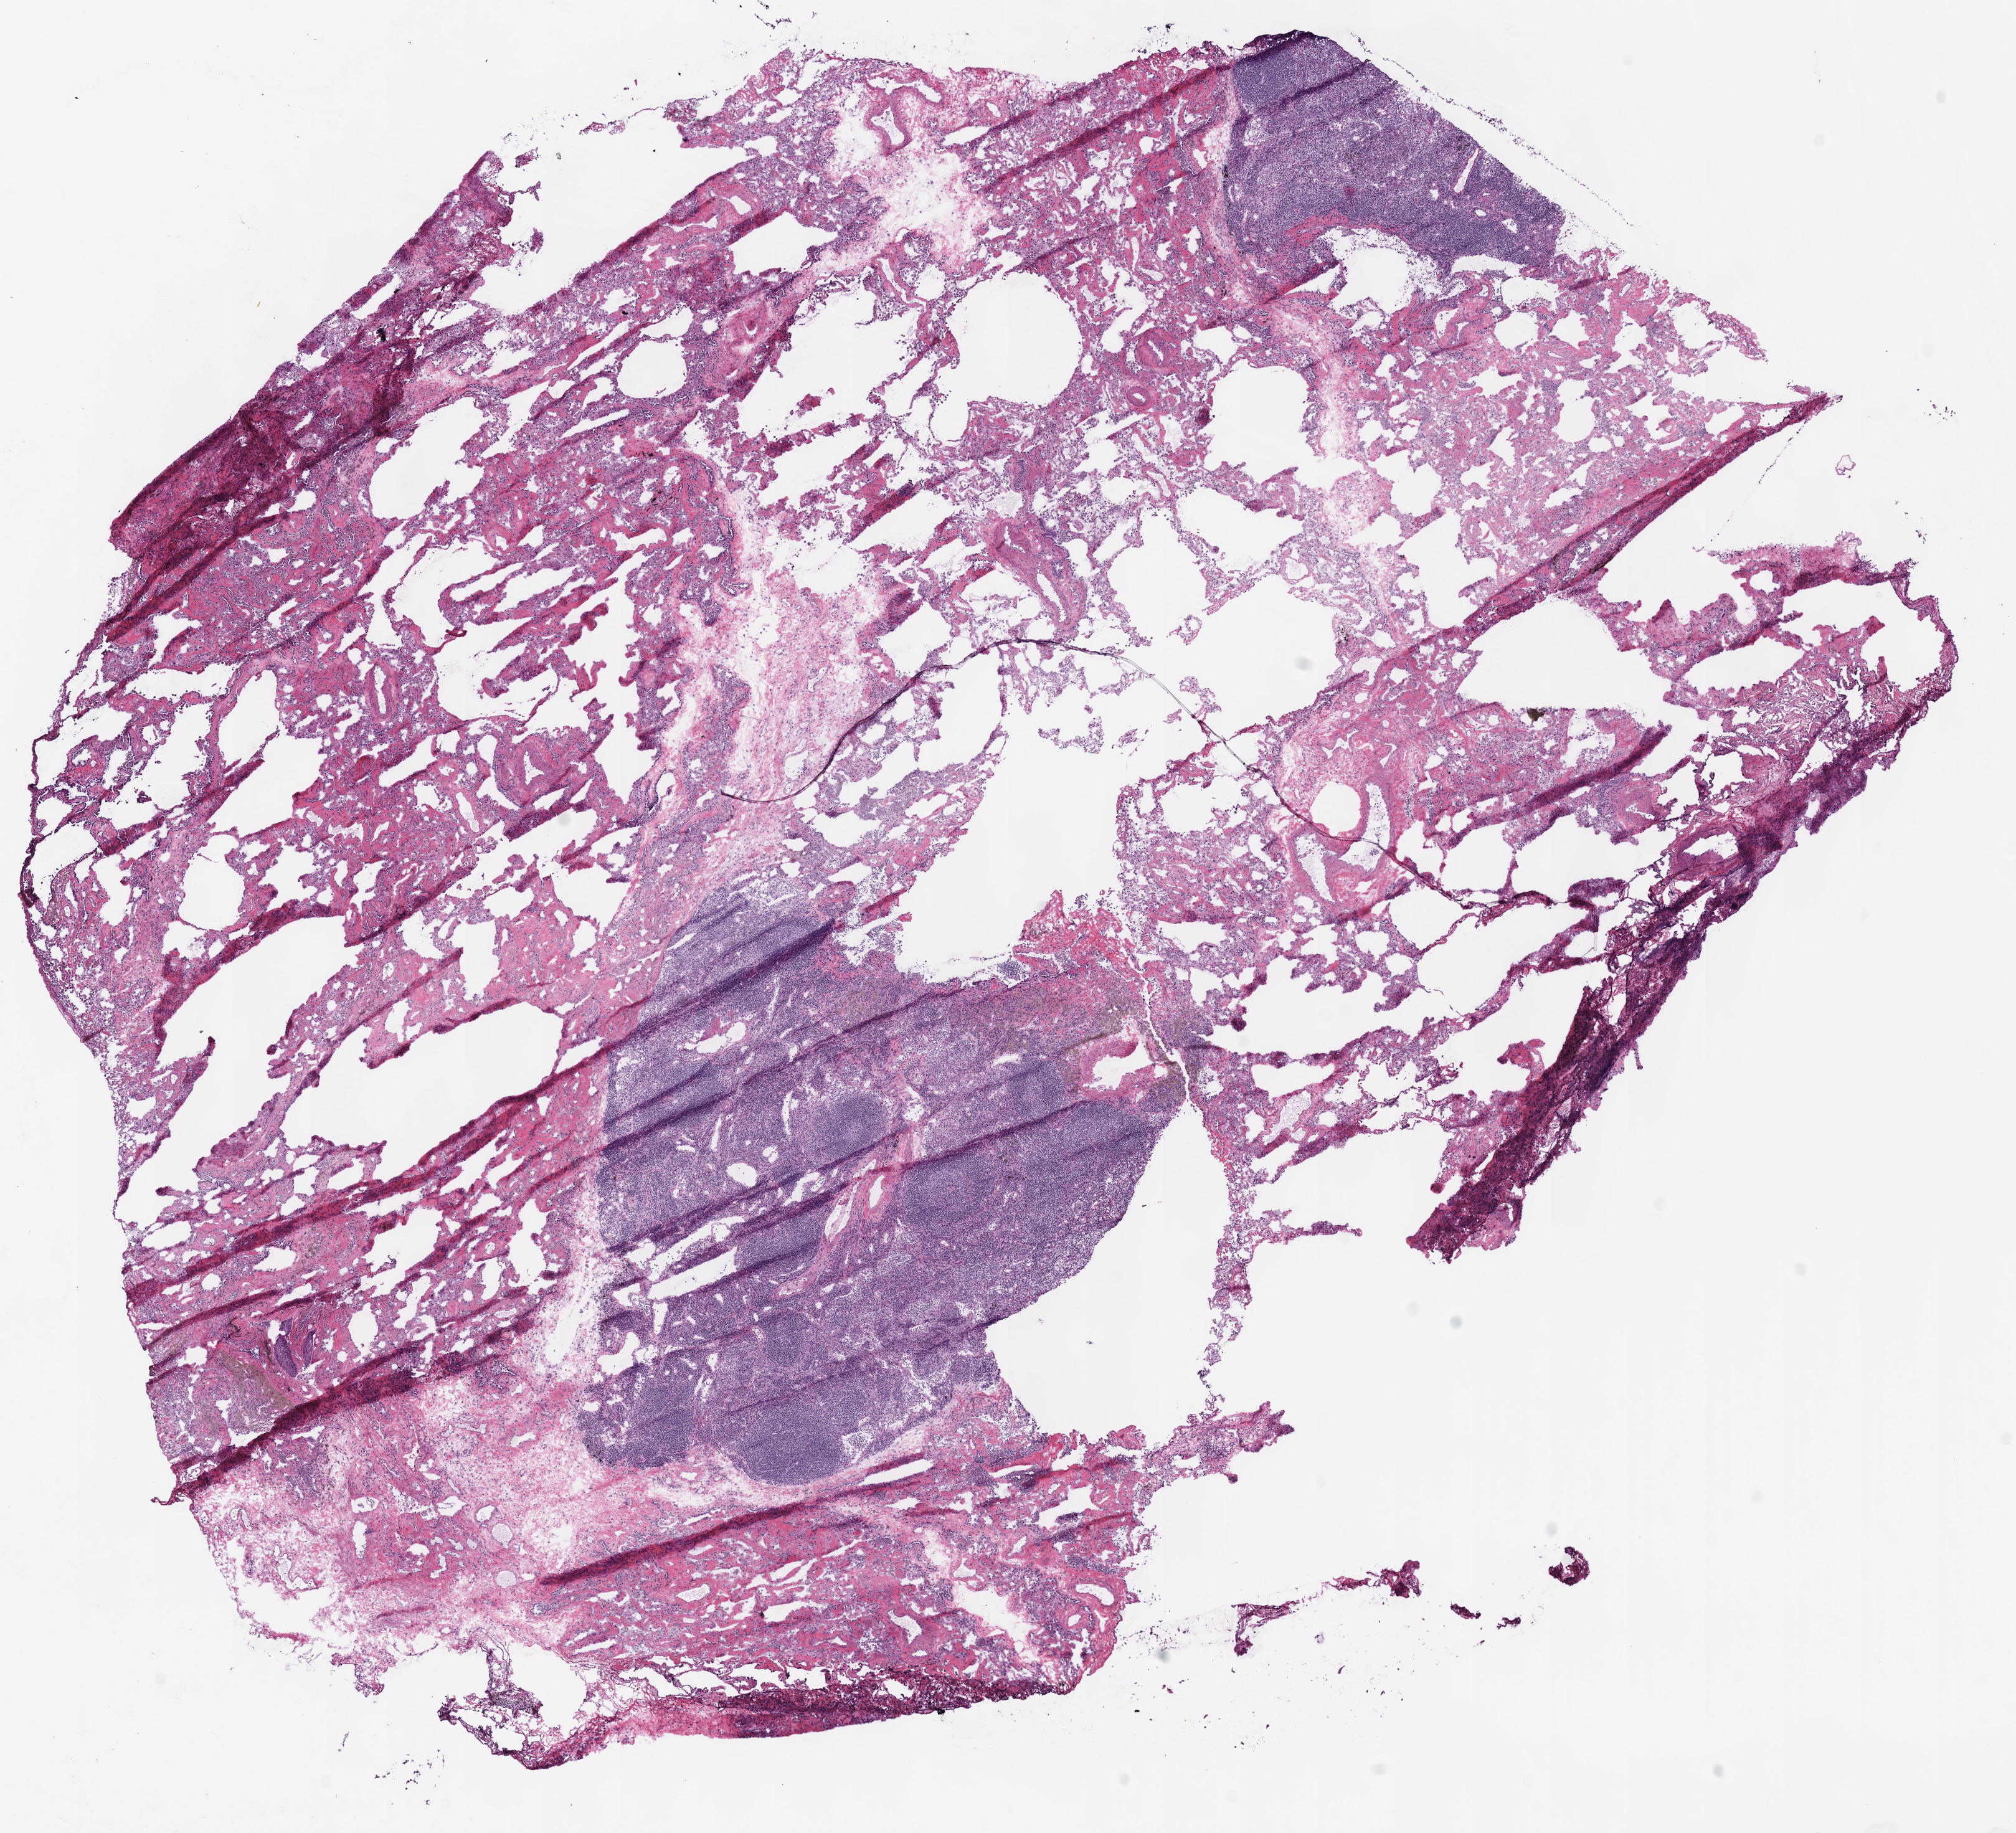
Digitized Hematoxylin and eosin (H&E) stained tissue section (whole slide), shown as a low-resolution overview of the whole scanned area (about 12.7 x 11.6 mm). Frozen section from the top of the tissue portion. Lung, solid tissue normal (non-tumour tissue) sample. Female patient; age at initial diagnosis 59 years. Inflammatory infiltration, as recorded: lymphocyte infiltration 35%, monocyte infiltration 20%, neutrophil infiltration 0%.
This section: solid tissue normal (non-tumour) sample from the same patient. Patient diagnosis: Squamous cell carcinoma, NOS (upper lobe, lung).